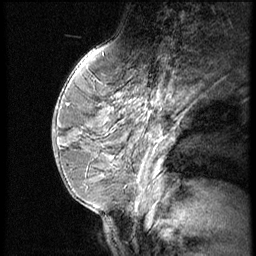
Breast MRI (dynamic contrast-enhanced), one sagittal slice. Position 22 of 62 along the scan axis. 3 images stored at this slice position (order not interpretable as contrast timing). 1.5 T. TE 4.2 ms, TR 9 ms. 2.5 mm slice thickness. 256 × 256 image matrix. Female patient, age 39 years. From the clinical record (not read from this slice): setting: breast cancer imaged before/during neoadjuvant chemotherapy; receptor status: triple-negative.
Annotated regions visible in this slice (semi-automatically segmented with operator editing):
- analysis volume of interest (the breast-tissue region the enhancement analysis was run in; not a lesion): bounding box (x1, y1, x2, y2) in pixels: (94, 70, 173, 156)
- tumour enhancement mask (voxels above the 140 % enhancement threshold inside the analysis volume of interest): (152, 103, 154, 106)